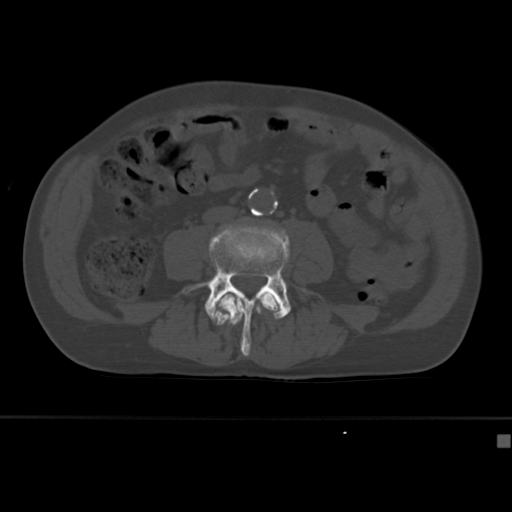
CT including the spine, one axial slice. Slice 112 of 430 in the series (ordered by position). 120 kVp. Bone window (W 1800 / L 400 HU). 512 × 512 image matrix, field of view 337 × 337 mm. Male patient, age 64 years. From the clinical record (not read from this slice): primary cancer: uterus.
Outlined on this slice (semi-automatic segmentation, software-assisted and operator-edited):
- L3 vertebra: box from (x=216, y=292) to (x=279, y=320) px
- L4 vertebra: (x=183, y=218)–(x=313, y=356)